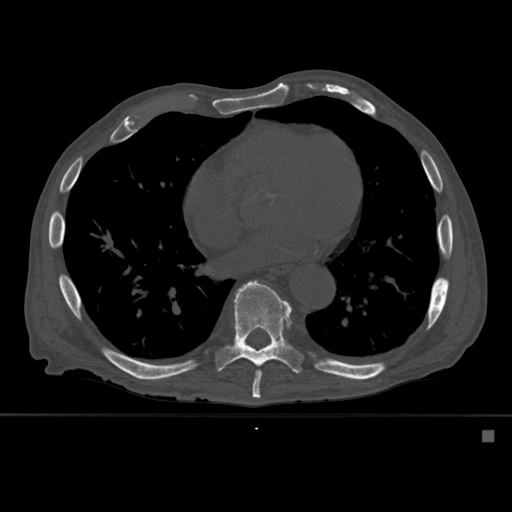
CT including the spine, one axial slice. Slice 336 of 527 in the series (ordered by position). Bone window (W 1800 / L 400 HU). 1.5 mm slice thickness. 512 × 512 image matrix, field of view 373 × 373 mm. Male patient, age 78 years. From the clinical record (not read from this slice): primary cancer: prostate.
Annotated regions visible in this slice (semi-automatic segmentation, software-assisted and operator-edited):
- T8 vertebra: bounding box (x1, y1, x2, y2) in pixels: (252, 371, 261, 398)
- T9 vertebra: (216, 280, 304, 386)